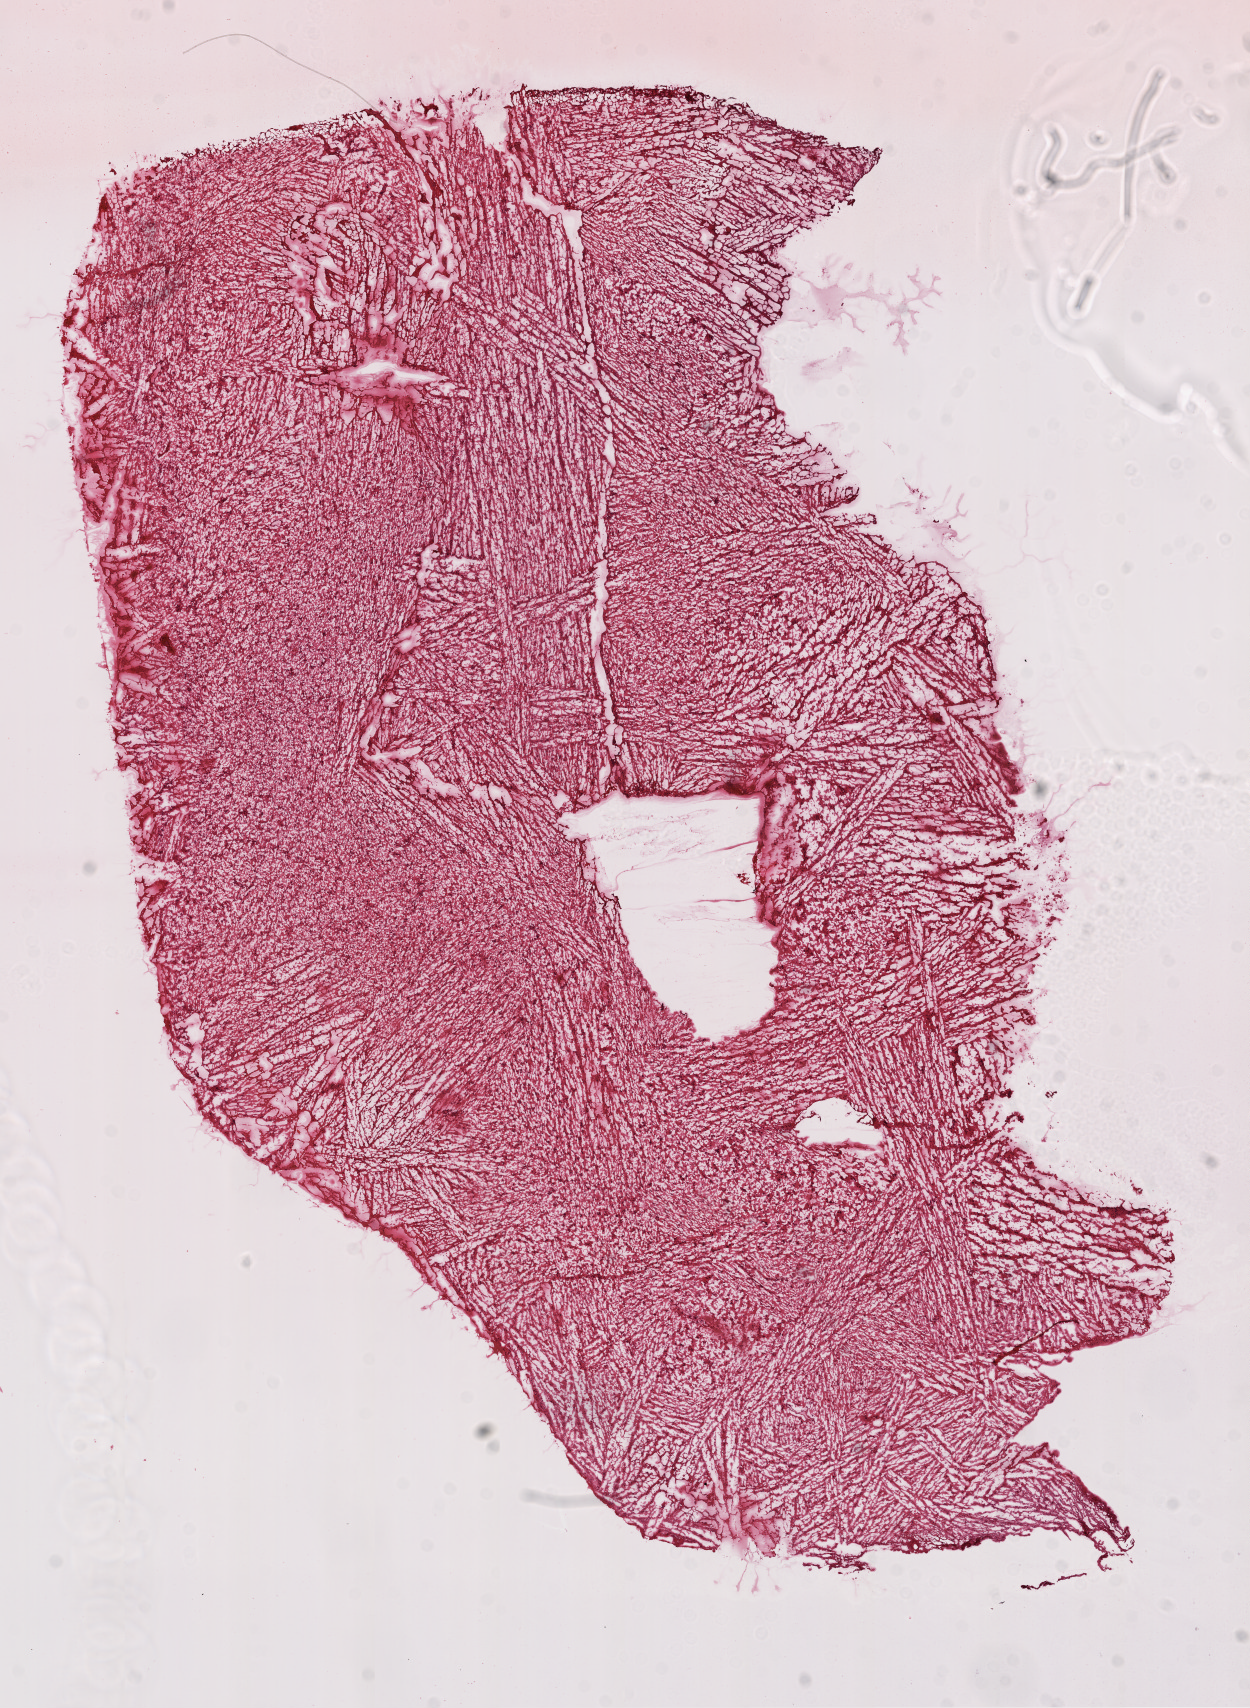
Whole-slide histology image, H&E-stained — whole scanned area (about 10.0 x 13.7 mm, from a 20x scan) shown as a low-resolution overview, frozen section, brain, primary tumour sample. Male, age 68 years at initial diagnosis. Pathologist review of this section (percent, as recorded): tumour cells 100%, tumour nuclei 70%, normal cells 0%, stromal cells 0%, necrosis 0%.
• pathologic diagnosis: Glioblastoma